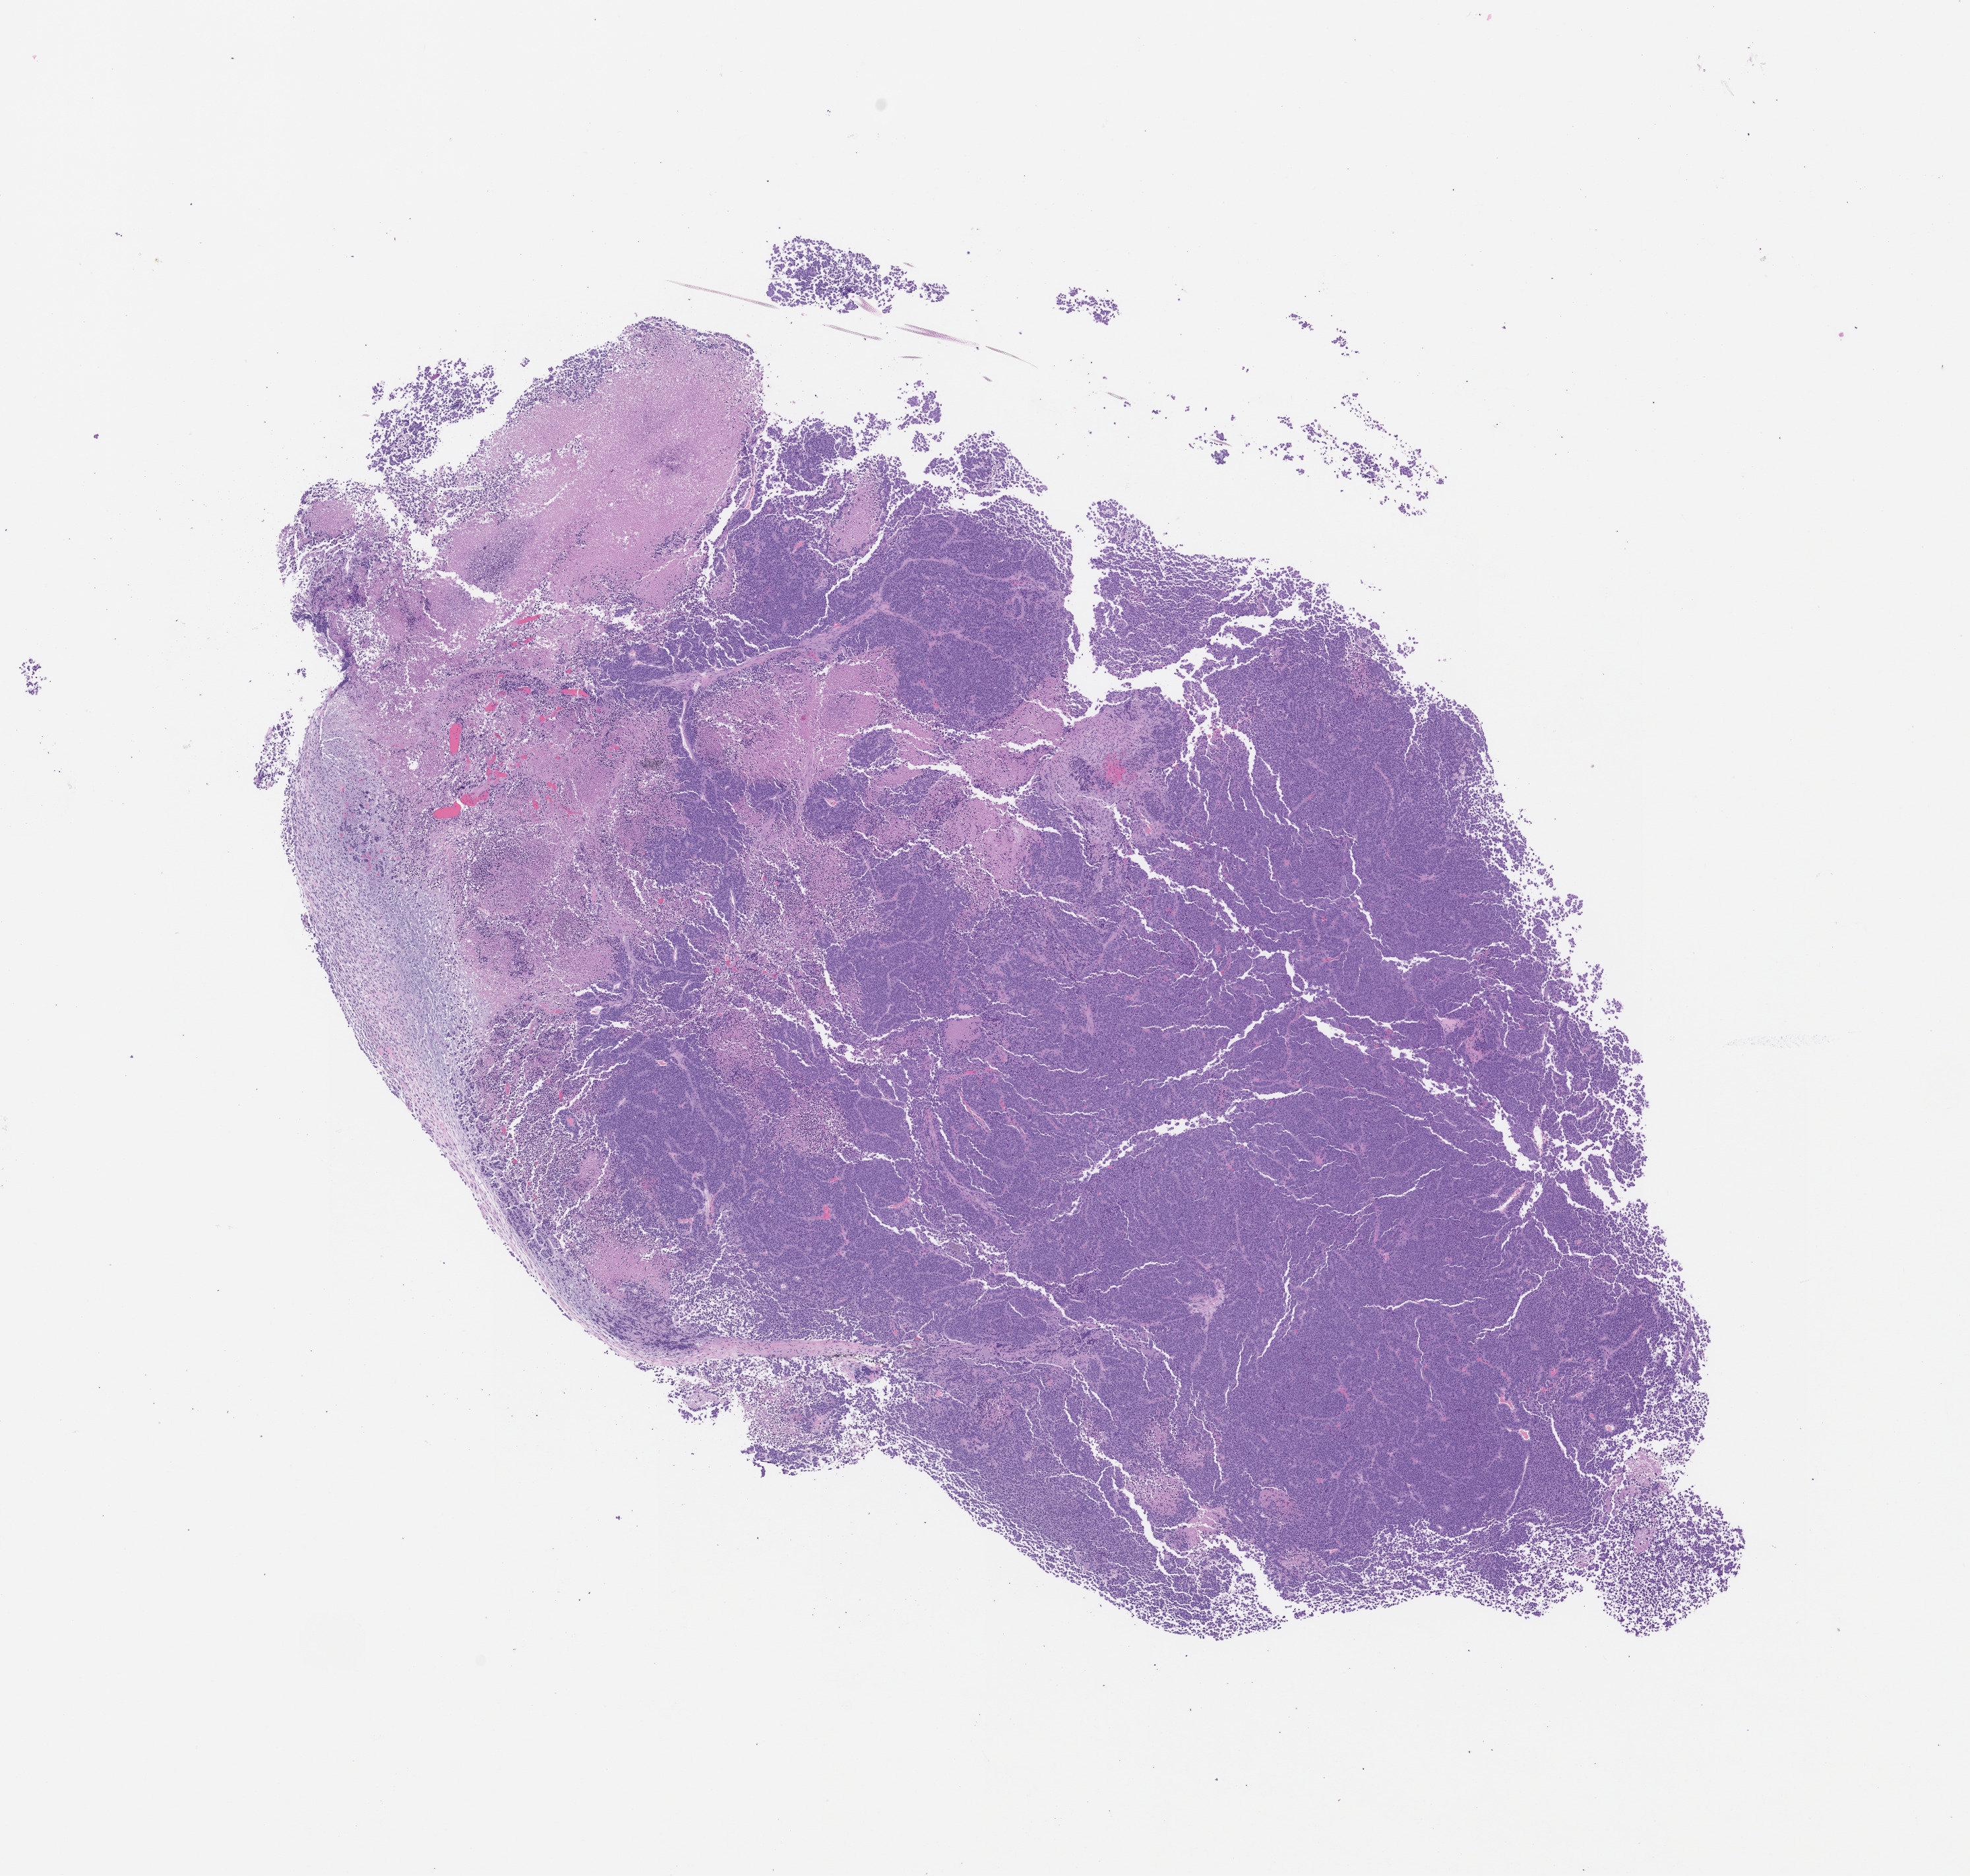
Whole-slide image, hematoxylin and eosin (H&E): patient-derived xenograft (human tumor grown in a mouse), passage 1 — a low-resolution overview of the entire scanned area, about 12.0 x 11.4 mm. Formalin-fixed, paraffin-embedded (FFPE) tissue. Originating tumor site category: bladder.
Originating patient diagnosis: Urothelial Carcinoma.